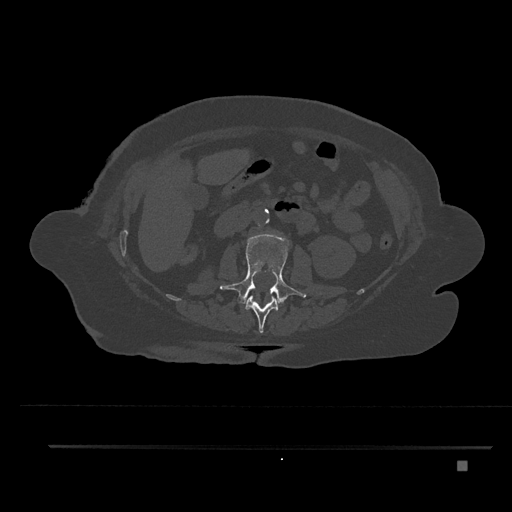
CT including the spine, one axial slice; slice 183 of 797 in the series (ordered by position); bone window (W 1800 / L 400 HU); 0.5 mm slice thickness; 512 × 512 image matrix, field of view 437 × 437 mm. Female patient, age 76 years. Case-level facts recorded for this patient, not image findings: primary cancer: lung; vertebrae with lytic lesions (as recorded): T11, L3.
Structures marked on this image (semi-automatically segmented with operator editing):
- L1 vertebra: bounding box [x1, y1, x2, y2] px = [245, 295, 280, 333]
- L2 vertebra: [220, 234, 306, 306]